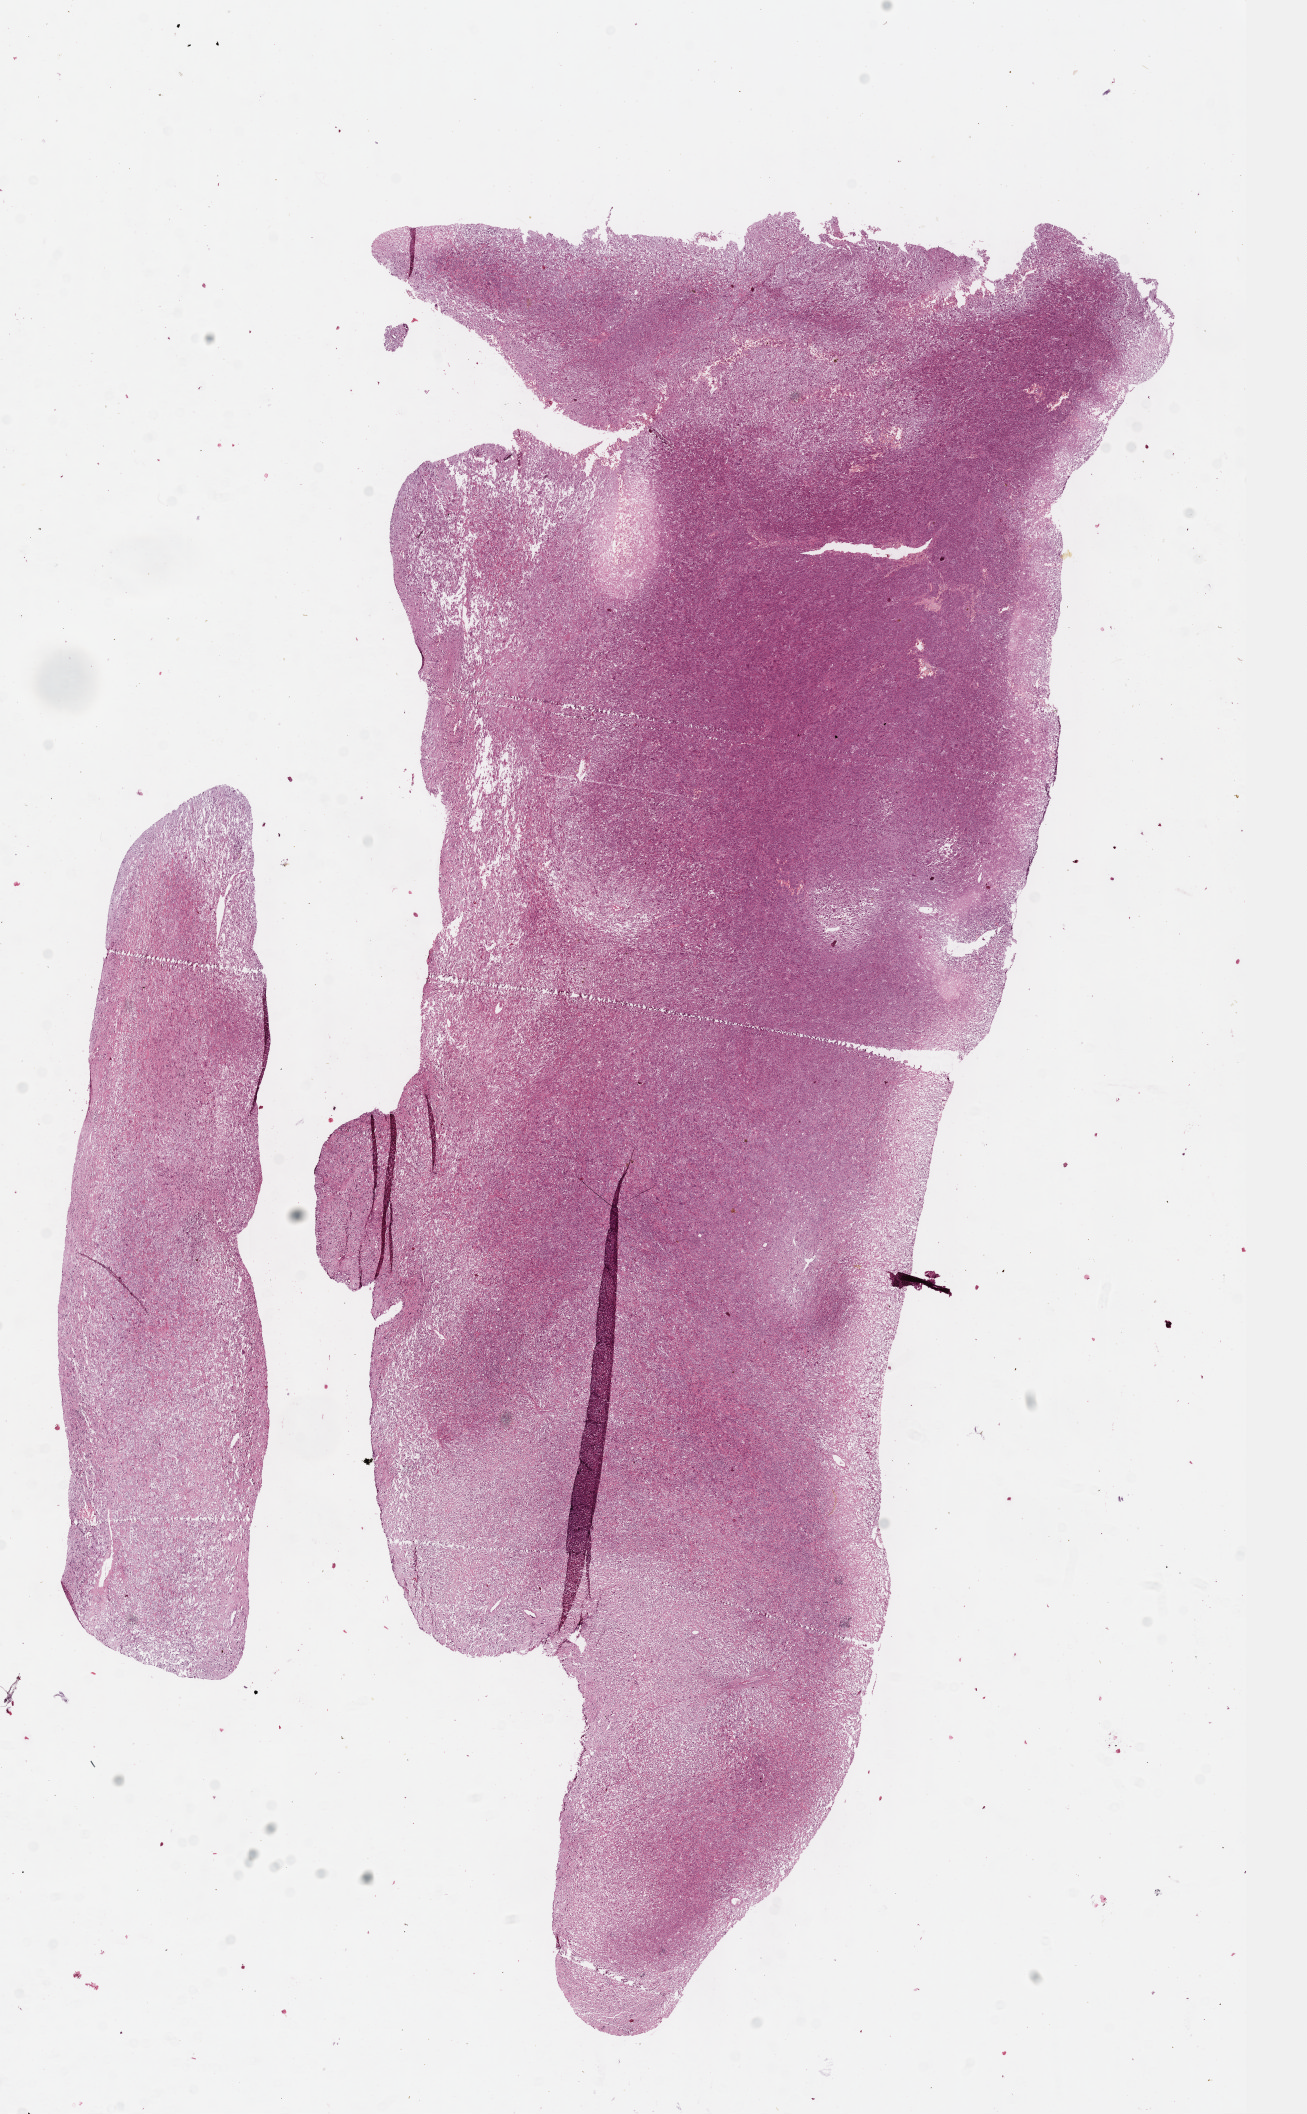
H&E-stained whole-slide image — whole scanned area (about 10.6 x 17.1 mm) shown as a low-resolution overview. FFPE section. Primary tumour sample from the liver. Male, age 56 years at initial diagnosis. Histologic grade: G3 (poorly differentiated).
AJCC pathologic stage: II. Histologic diagnosis: Hepatocellular carcinoma, NOS.